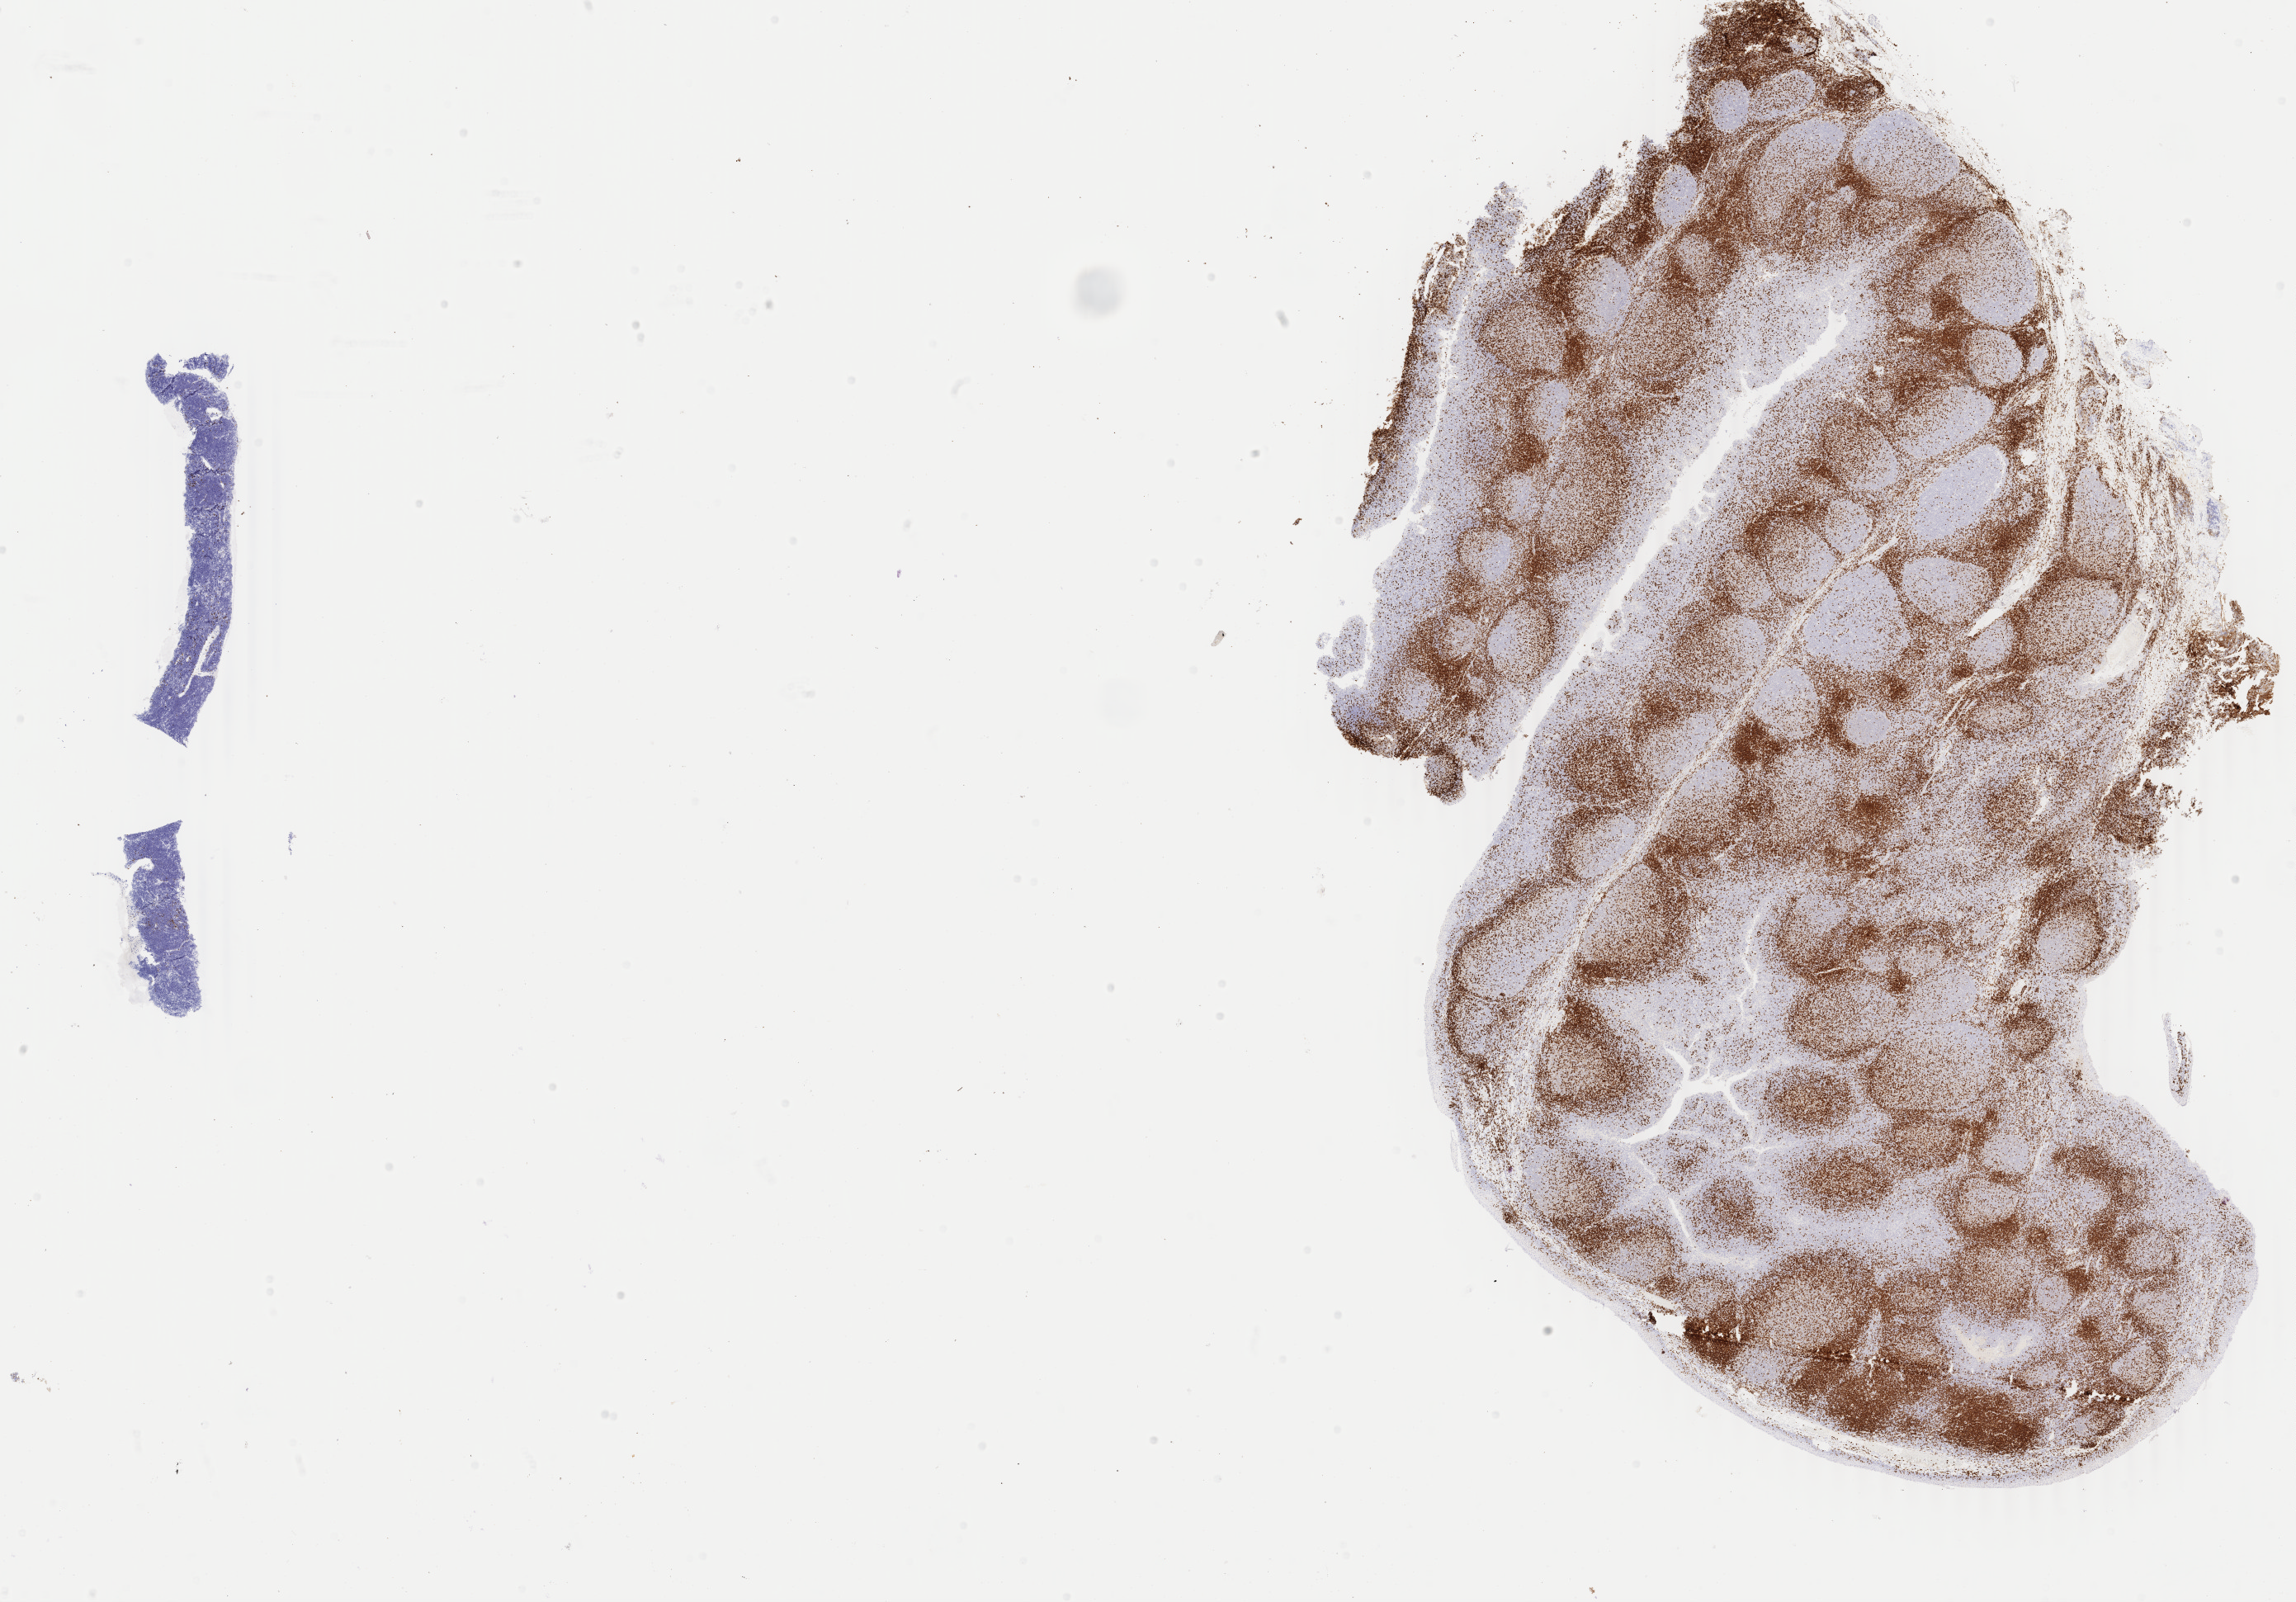
Immunohistochemistry (IHC) whole-slide image stained for CD3, low-resolution overview of the scanned area, about 22.1 x 15.4 mm. Tumor tissue. Site: abdominal lymph node. Female patient; age at initial diagnosis 6 years.
Histologic diagnosis: Burkitt lymphoma, NOS.